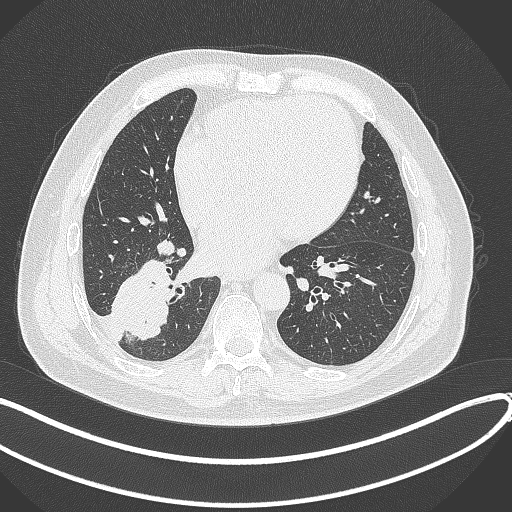
Chest CT, one axial slice; position 140 of 360 along the scan axis; reconstruction kernel B70f; lung window (W 1500 / L -600 HU); 512 × 512 image matrix, field of view 400 × 400 mm. Patient: male, 59 years.
Structures marked on this image (rectangle marked by the reading radiologist):
- lung tumour (recorded histology: adenocarcinoma): box from (x=108, y=256) to (x=179, y=338) px